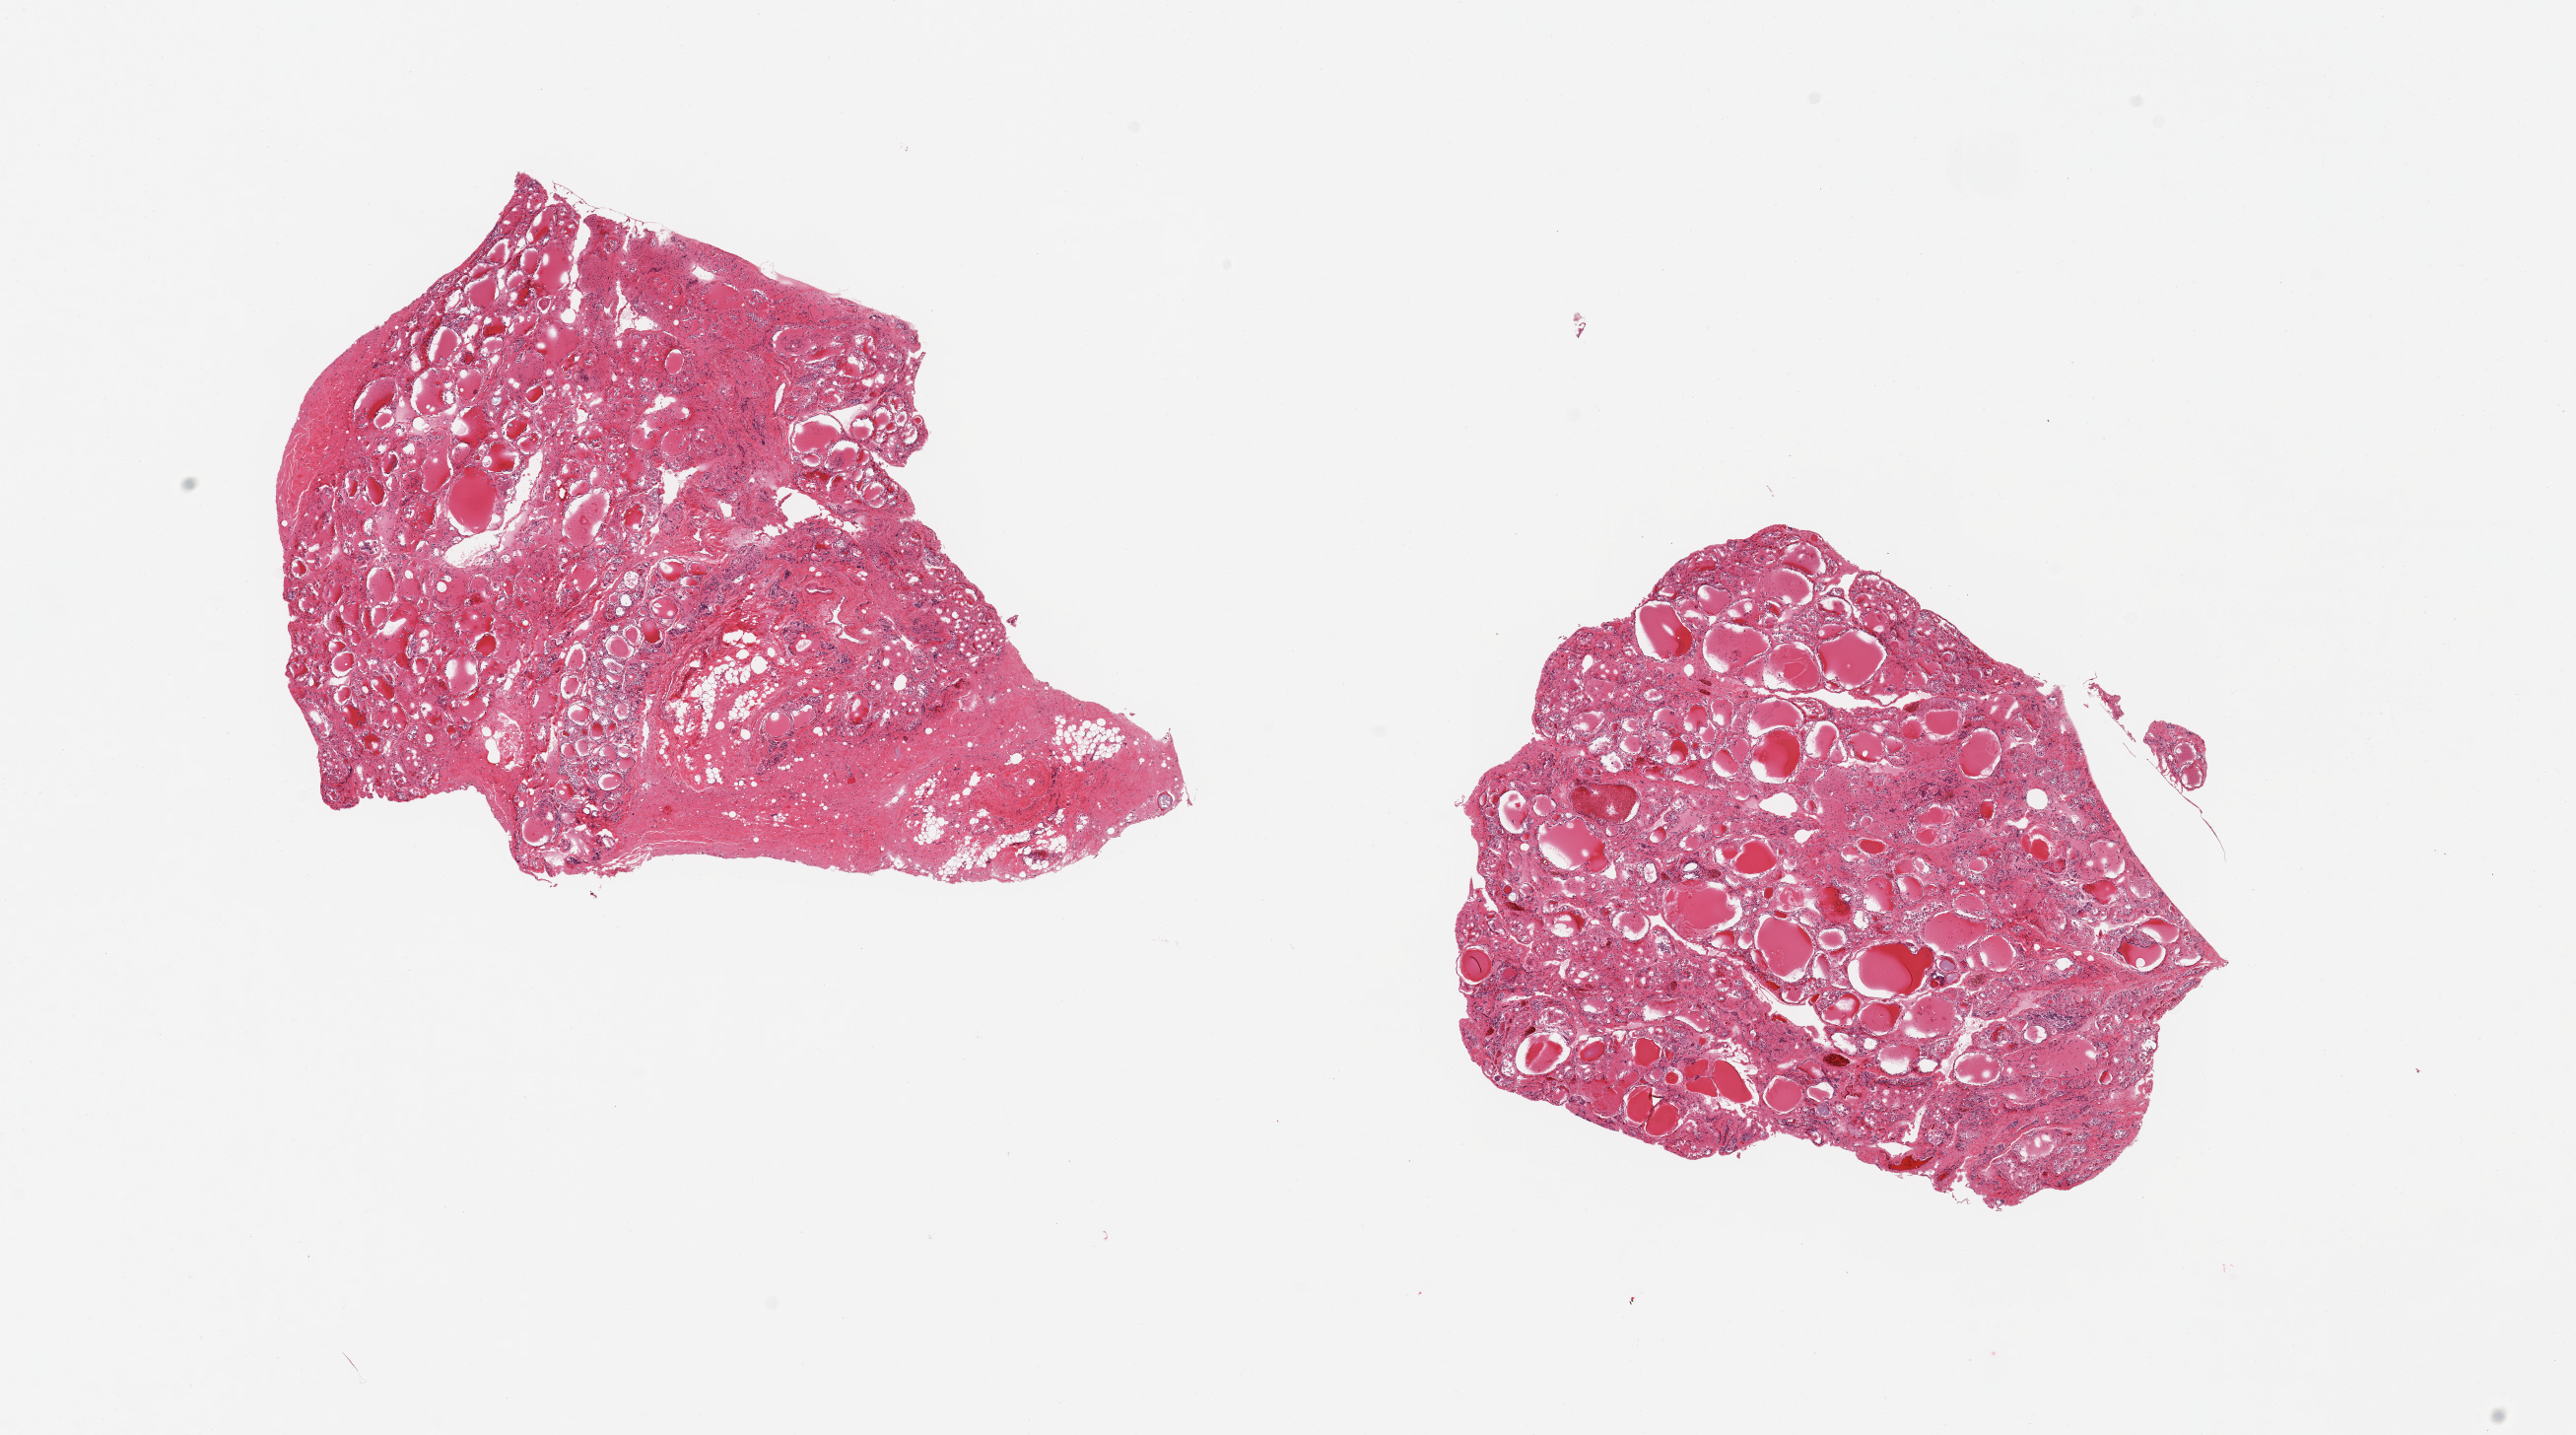
Digitized hematoxylin and eosin (H&E)-stained section, a low-resolution overview of the entire scanned area, about 20.7 x 11.5 mm; PAXgene-fixed, paraffin-embedded tissue; section of thyroid (target tissue); tissue donor sample.
Reviewer comment on this tissue sample: 2 pieces; 1 has 20% internal & external fibrofatty tissue [in part].